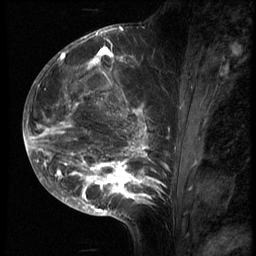
Breast MRI (dynamic contrast-enhanced), one sagittal slice. 3 images stored at this slice position (order not interpretable as contrast timing). 1.5 T. TE 4.2 ms, TR 9 ms. 2.5 mm slice thickness. 256 × 256 image matrix. Female patient, age 28 years. From the clinical record (not read from this slice): setting: breast cancer imaged before/during neoadjuvant chemotherapy.
Outlined on this slice (semi-automatically segmented with operator editing):
- analysis volume of interest (the breast-tissue region the enhancement analysis was run in; not a lesion): bounding box (x1, y1, x2, y2) in pixels: (43, 42, 178, 215)
- tumour enhancement mask (voxels above the 140 % enhancement threshold inside the analysis volume of interest): (43, 48, 167, 208)